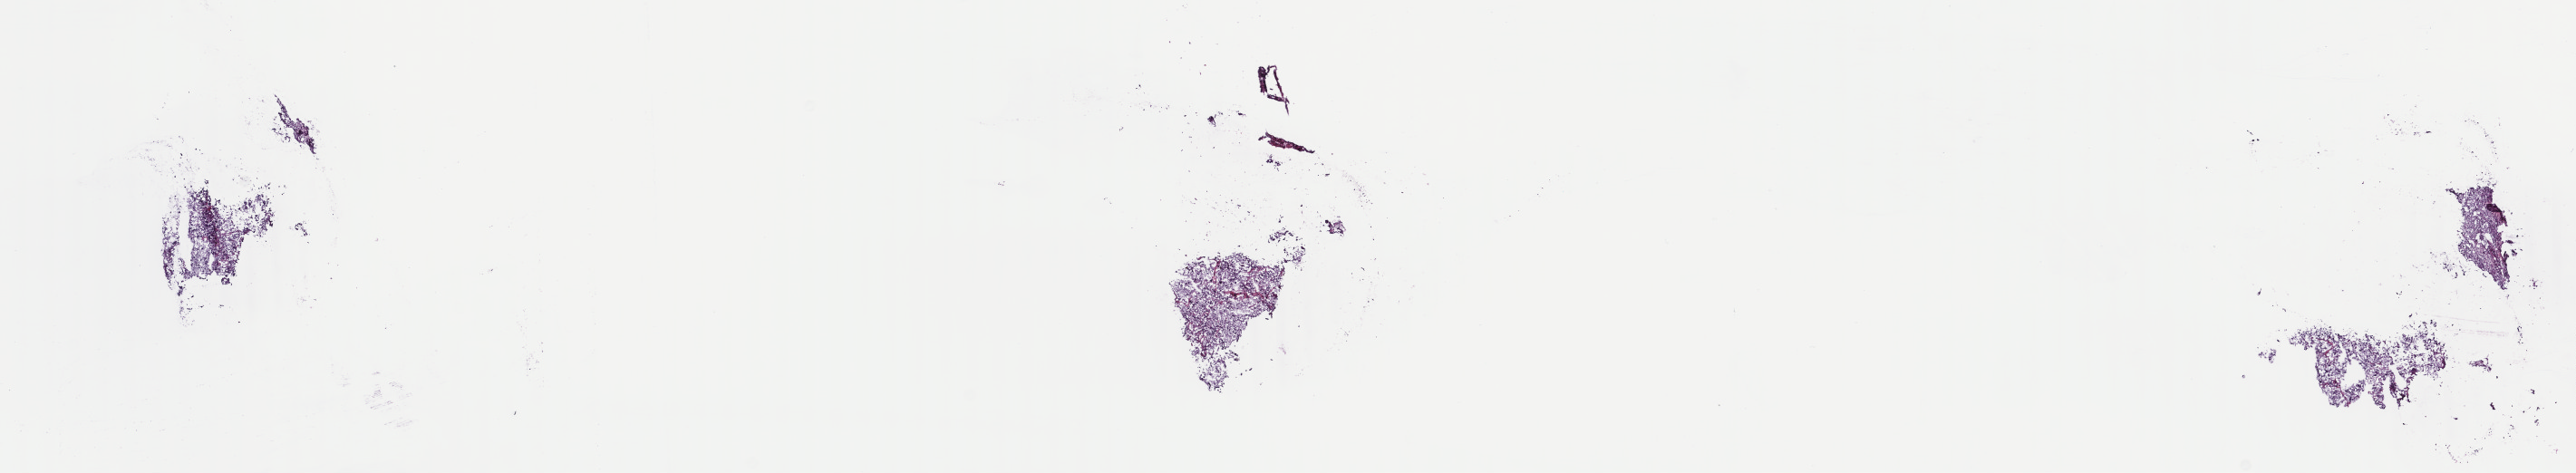
Whole-slide histology image, Hematoxylin and eosin (H&E) stained, whole scanned area (about 22.6 x 4.2 mm, from a 40x scan) shown as a low-resolution overview, frozen section from the top of the tissue portion, primary tumour sample from the adrenal gland. Male, age 54 years at initial diagnosis. Pathologist review of this section (percent, as recorded): tumour cells 100%, tumour nuclei 85%, normal cells 0%, stromal cells 0%, necrosis 0%. Inflammatory infiltration, as recorded: lymphocyte infiltration 0%, monocyte infiltration 0%, neutrophil infiltration 0%.
Laterality: left. Diagnosis: Pheochromocytoma, NOS.